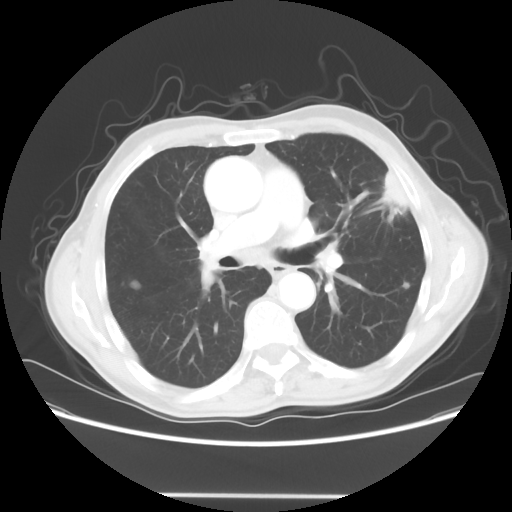
Chest CT, one axial slice. Position 36 of 64 along the scan axis. Reconstruction kernel STANDARD. 120 kVp. Lung window (W 1500 / L -600 HU). 5 mm slice thickness. 512 × 512 image matrix, field of view 392 × 392 mm. Male patient, age 71 years. From the clinical record (not read from this slice): clinical TNM (as recorded): T1c N0 M0; histopathological grade: G2-3.
Structures marked on this image (rectangle marked by the reading radiologist):
- lung tumour (recorded histology: adenocarcinoma): bounding box (x1, y1, x2, y2) in pixels: (375, 164, 418, 230)